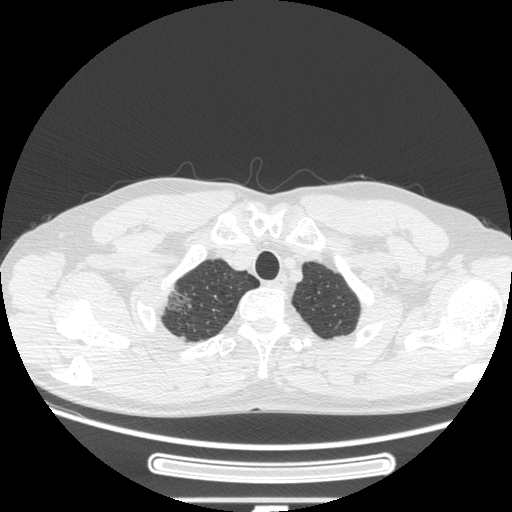
Chest CT, one axial slice. 120 kVp. Lung window (W 1500 / L -600 HU). 1.25 mm slice thickness. 512 × 512 image matrix. Male patient, age 53 years. Case-level facts recorded for this patient, not image findings: clinical TNM (as recorded): T1c N0 M0; histopathological grade: G2.
Structures marked on this image (bounding box drawn by a radiologist):
- lung tumour (recorded histology: adenocarcinoma): bounding box [x1, y1, x2, y2] px = [157, 282, 193, 326]